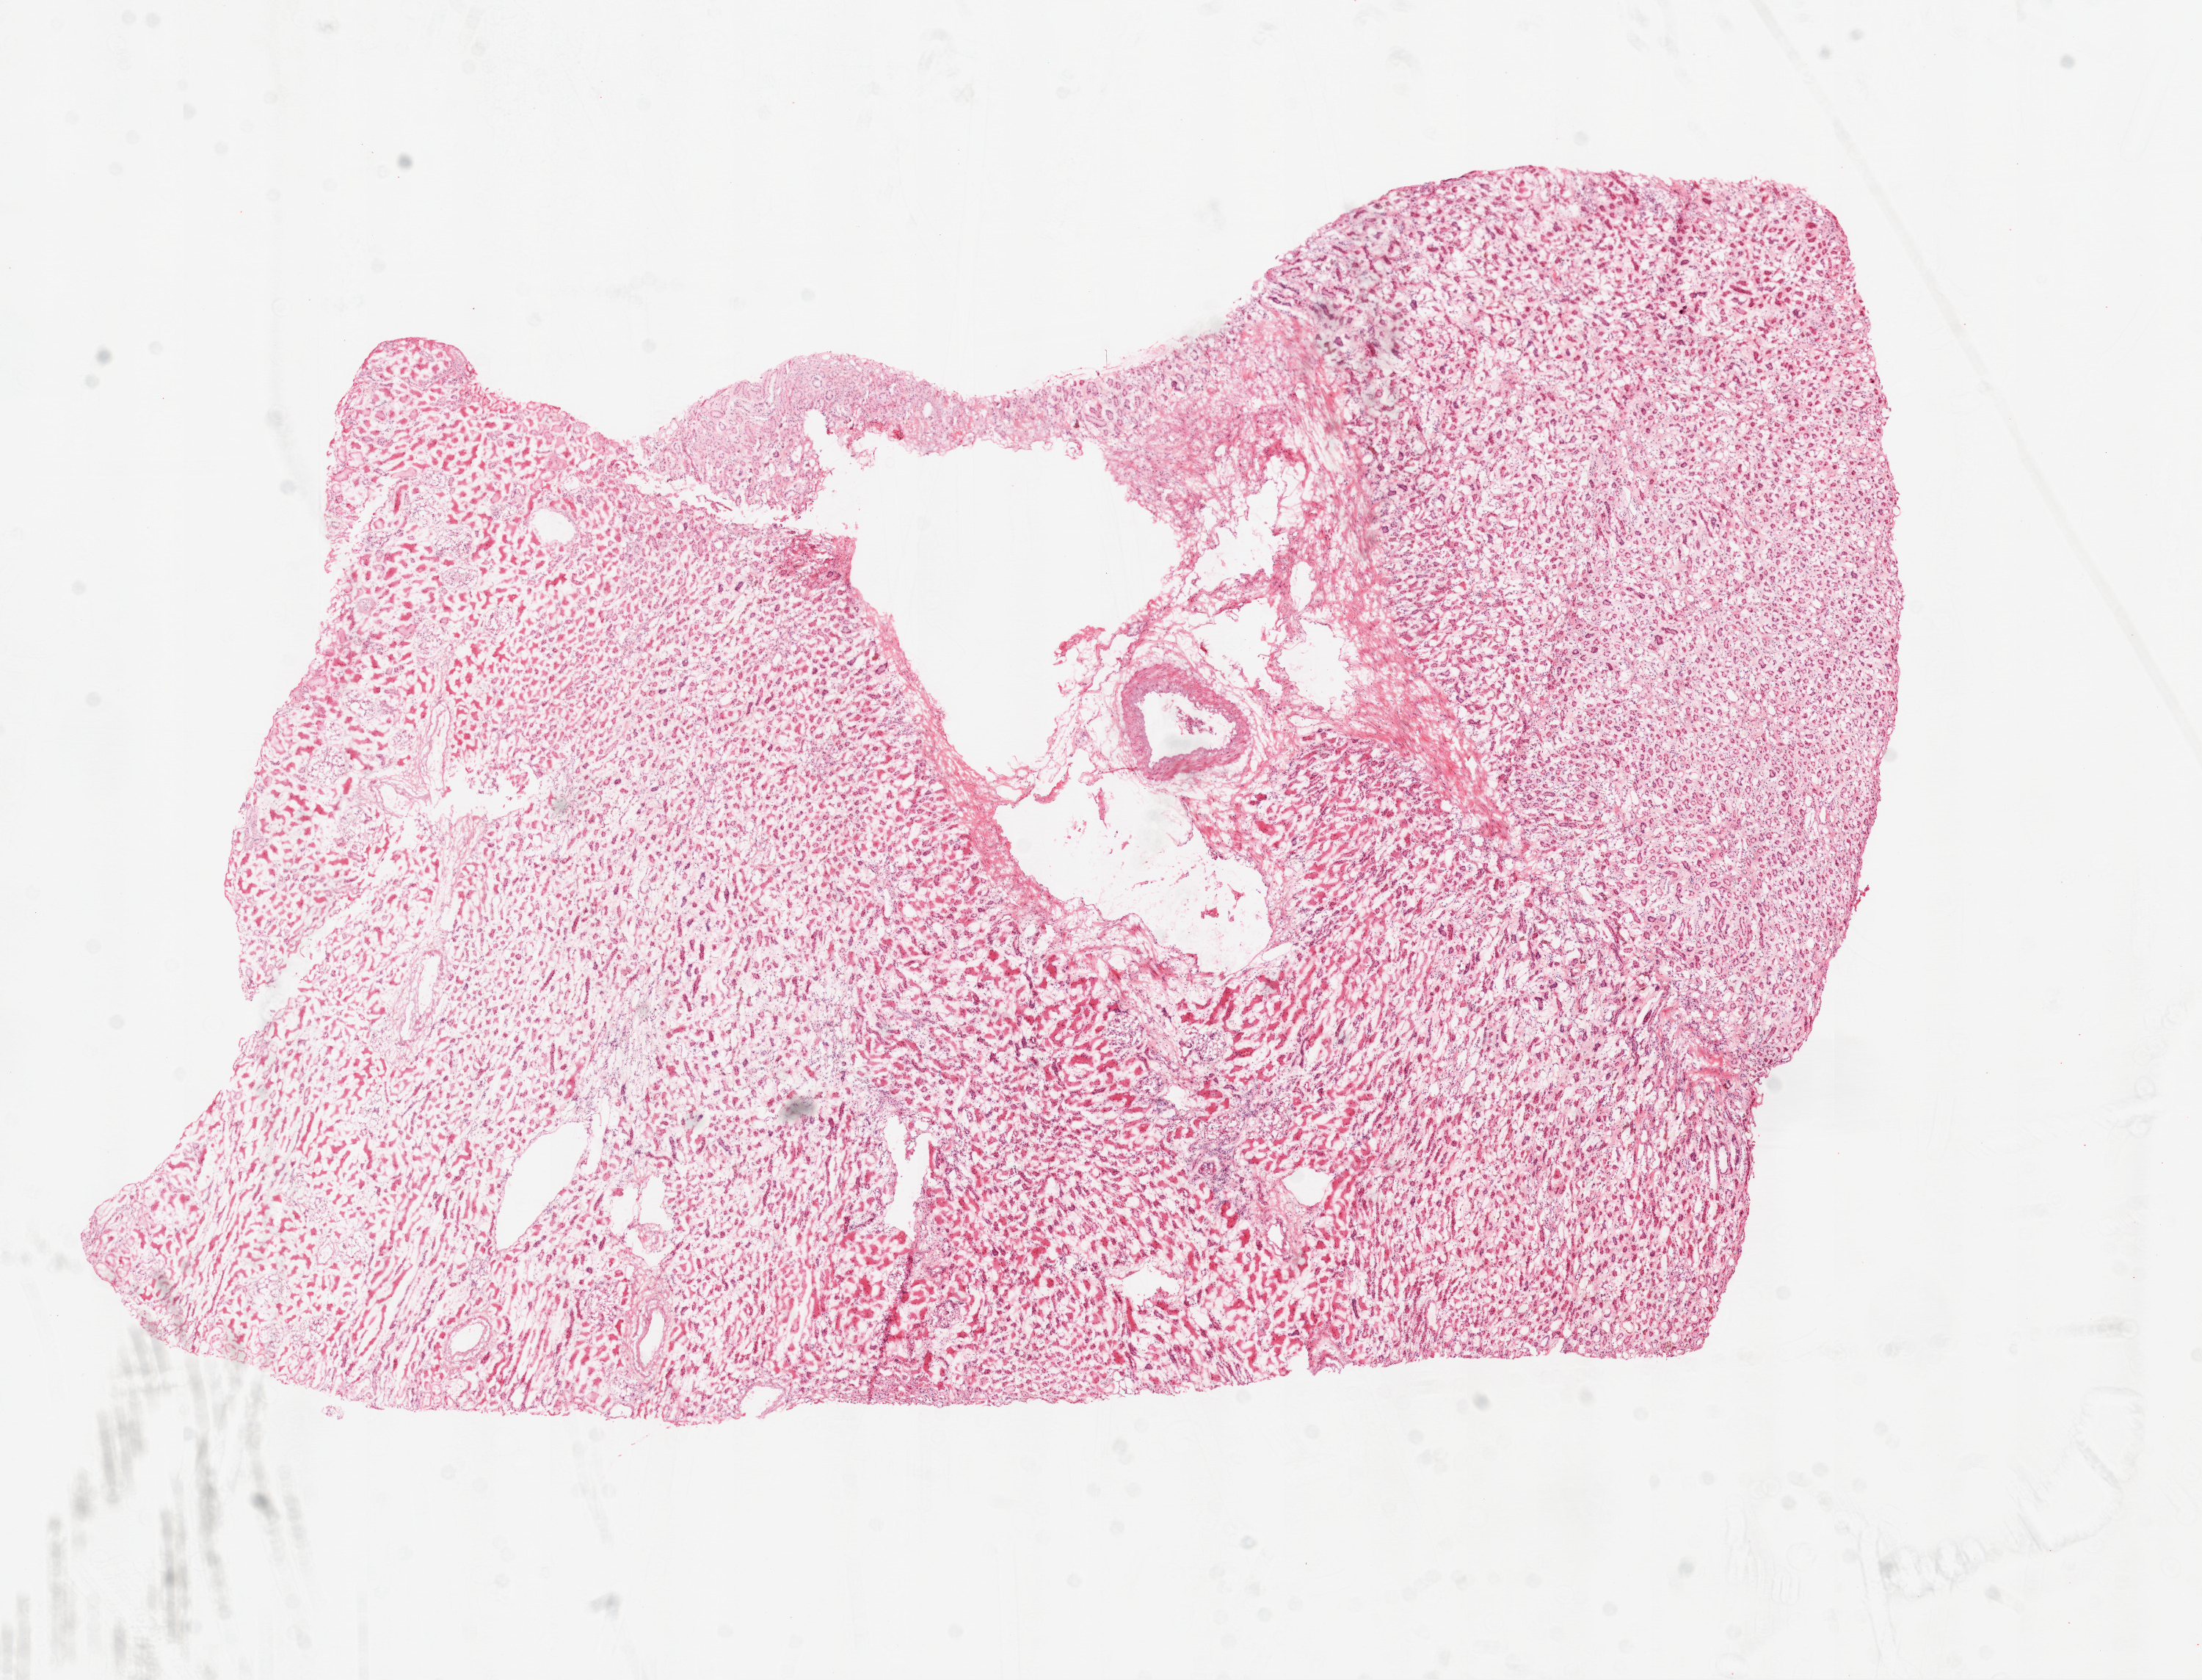
H&E whole-slide image, shown as a low-resolution overview of the whole scanned area (about 12.0 x 9.2 mm), frozen section, kidney, solid tissue normal (non-tumour tissue) sample. Female, age 59 years at initial diagnosis.
• this section: solid tissue normal (non-tumour) sample from the same patient
• patient diagnosis: Clear cell adenocarcinoma, NOS